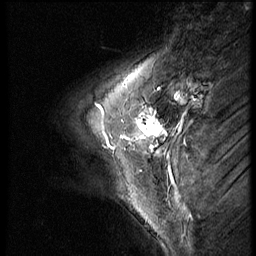
Breast MRI (dynamic contrast-enhanced), one sagittal slice; position 15 of 56 along the scan axis; dynamic contrast-enhanced series, image 2 of 3 at this slice position (ordered by acquisition); 1.5 T; TE 4.2 ms, TR 9 ms; 2.5 mm slice thickness; 256 × 256 image matrix, field of view 180 × 180 mm. Patient: female, 46 years. From the clinical record (not read from this slice): setting: breast cancer imaged before/during neoadjuvant chemotherapy; receptor status: HER2-positive.
Outlined on this slice (semi-automatically segmented with operator editing):
- analysis volume of interest (the breast-tissue region the enhancement analysis was run in; not a lesion): bounding box (x1, y1, x2, y2) in pixels: (65, 98, 174, 182)
- tumour enhancement mask (voxels above the 140 % enhancement threshold inside the analysis volume of interest): (103, 108, 165, 149)